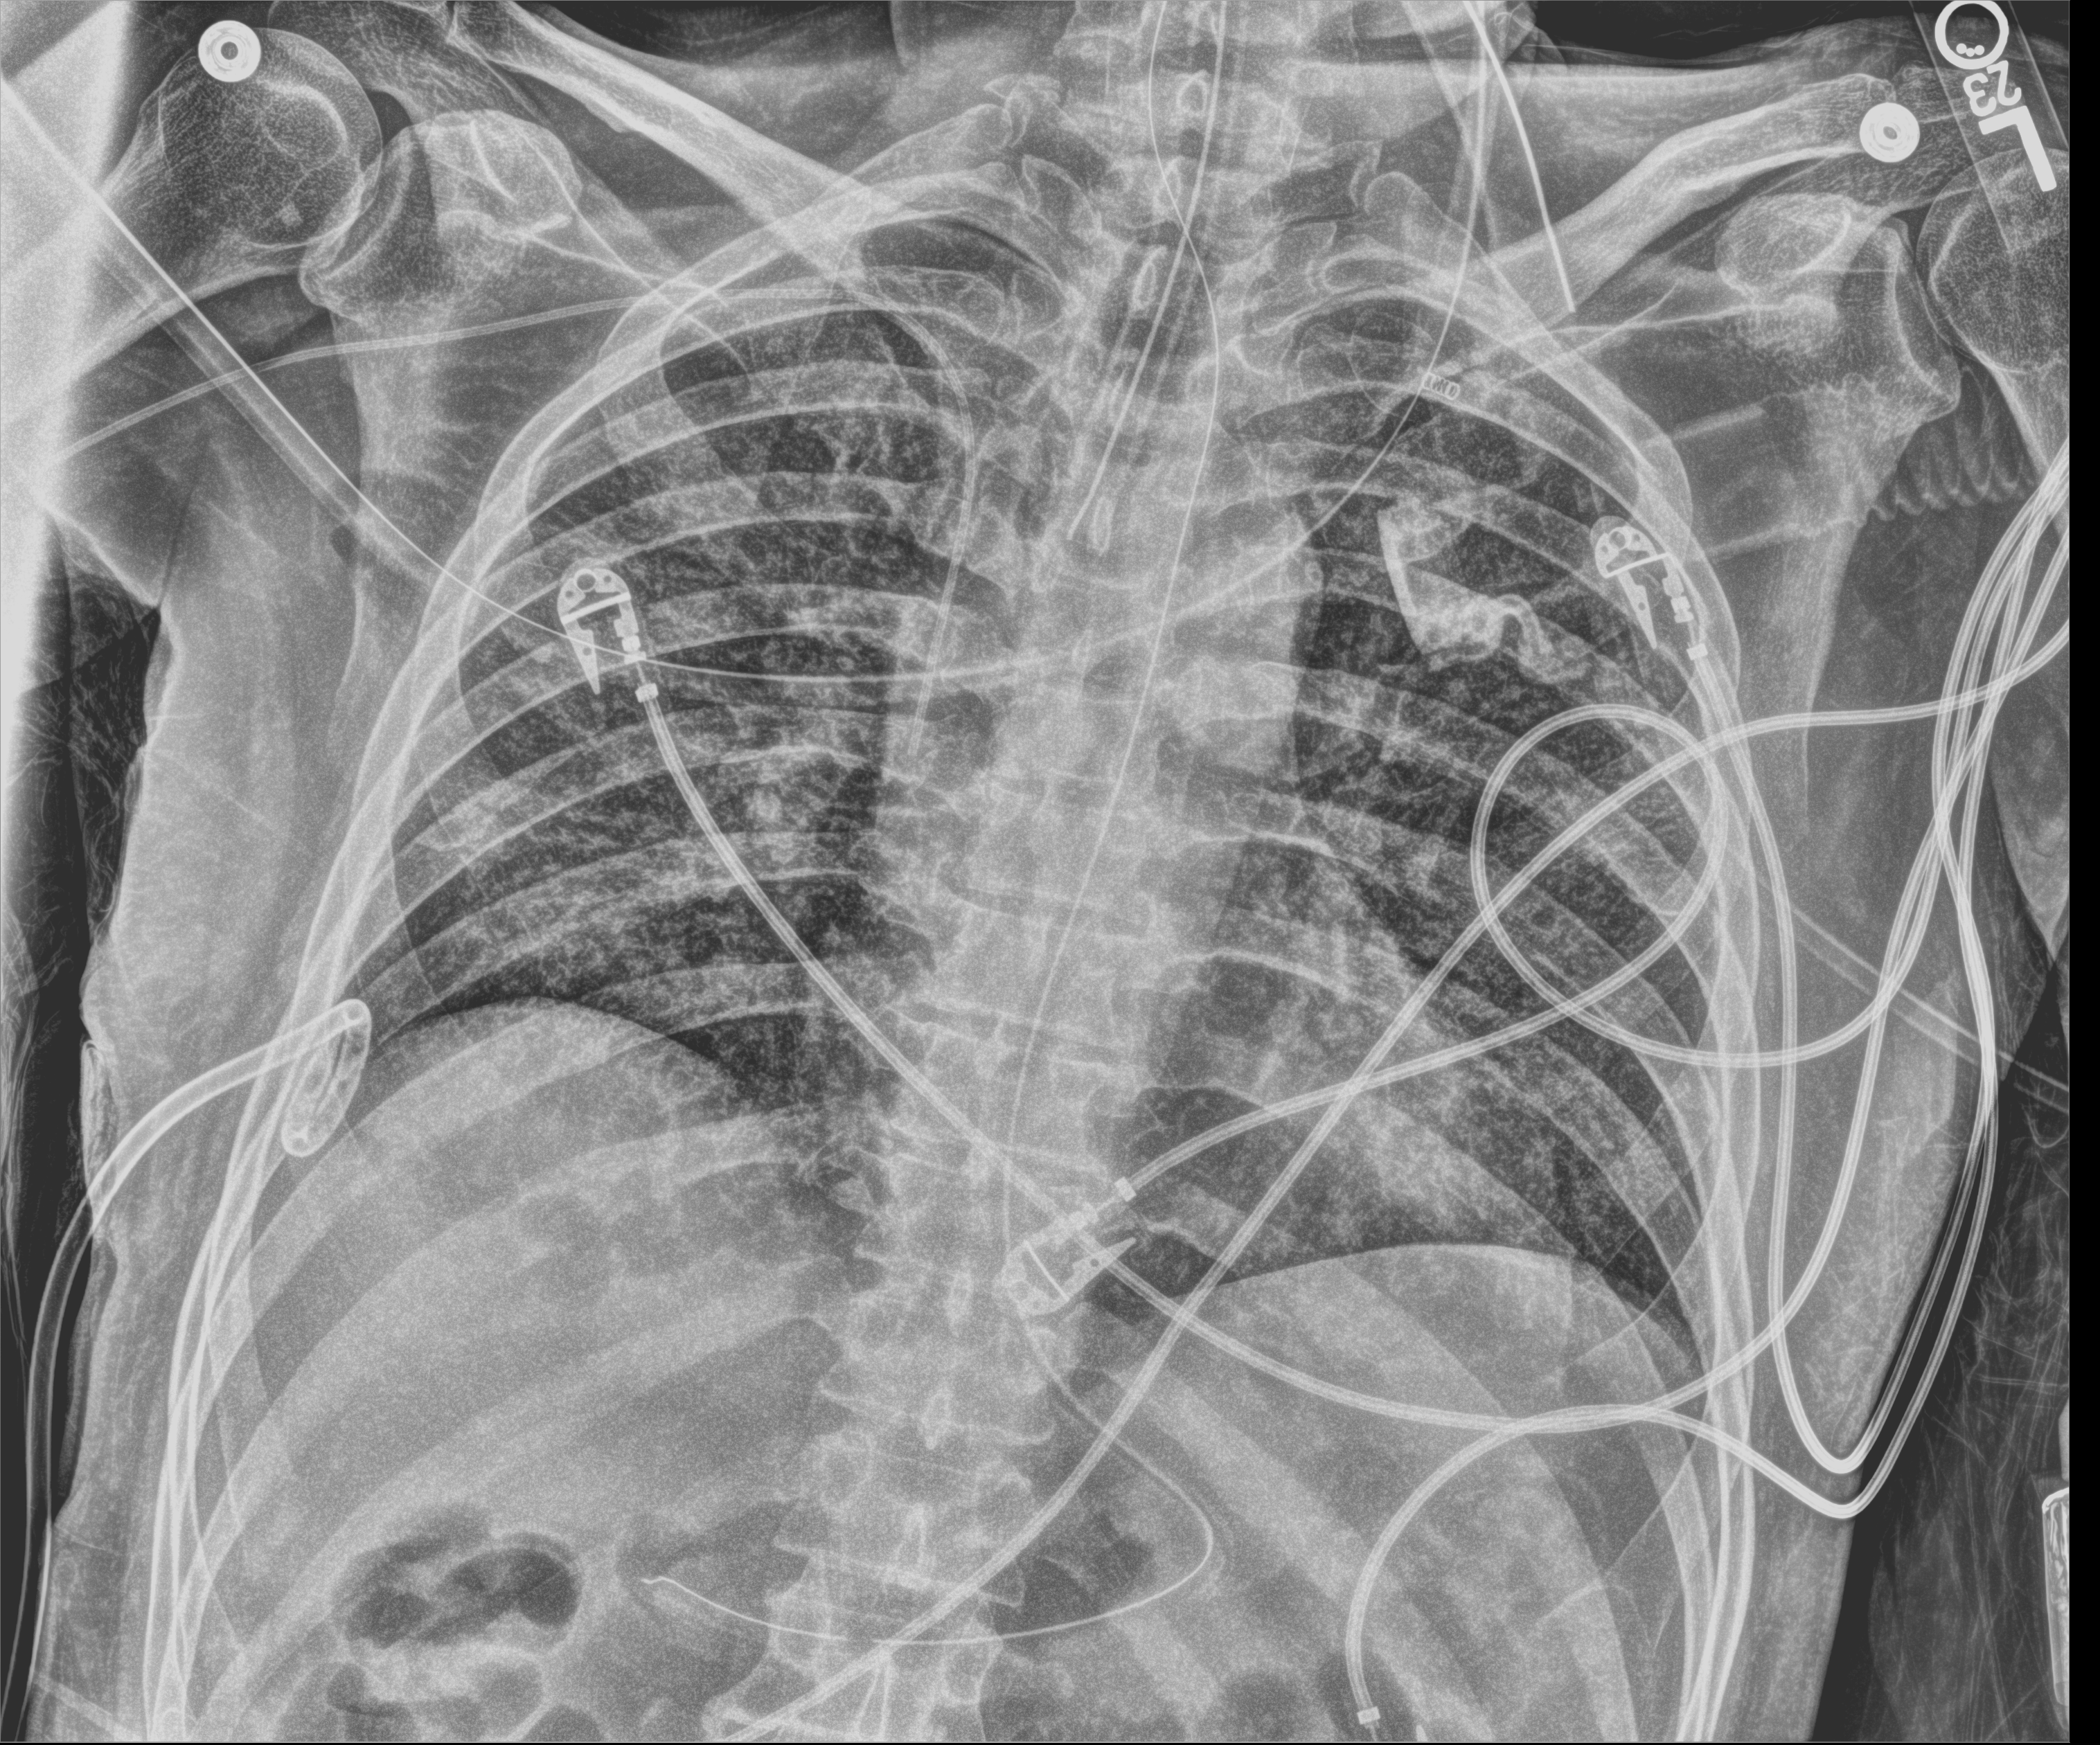
Portable chest radiograph, anteroposterior (AP) projection. Patient hospitalised with COVID-19; male, aged 18–59 years.
Admission-level facts for this patient (not findings on this image; timing relative to this image not recorded): admitted to intensive care during this hospital stay: yes.